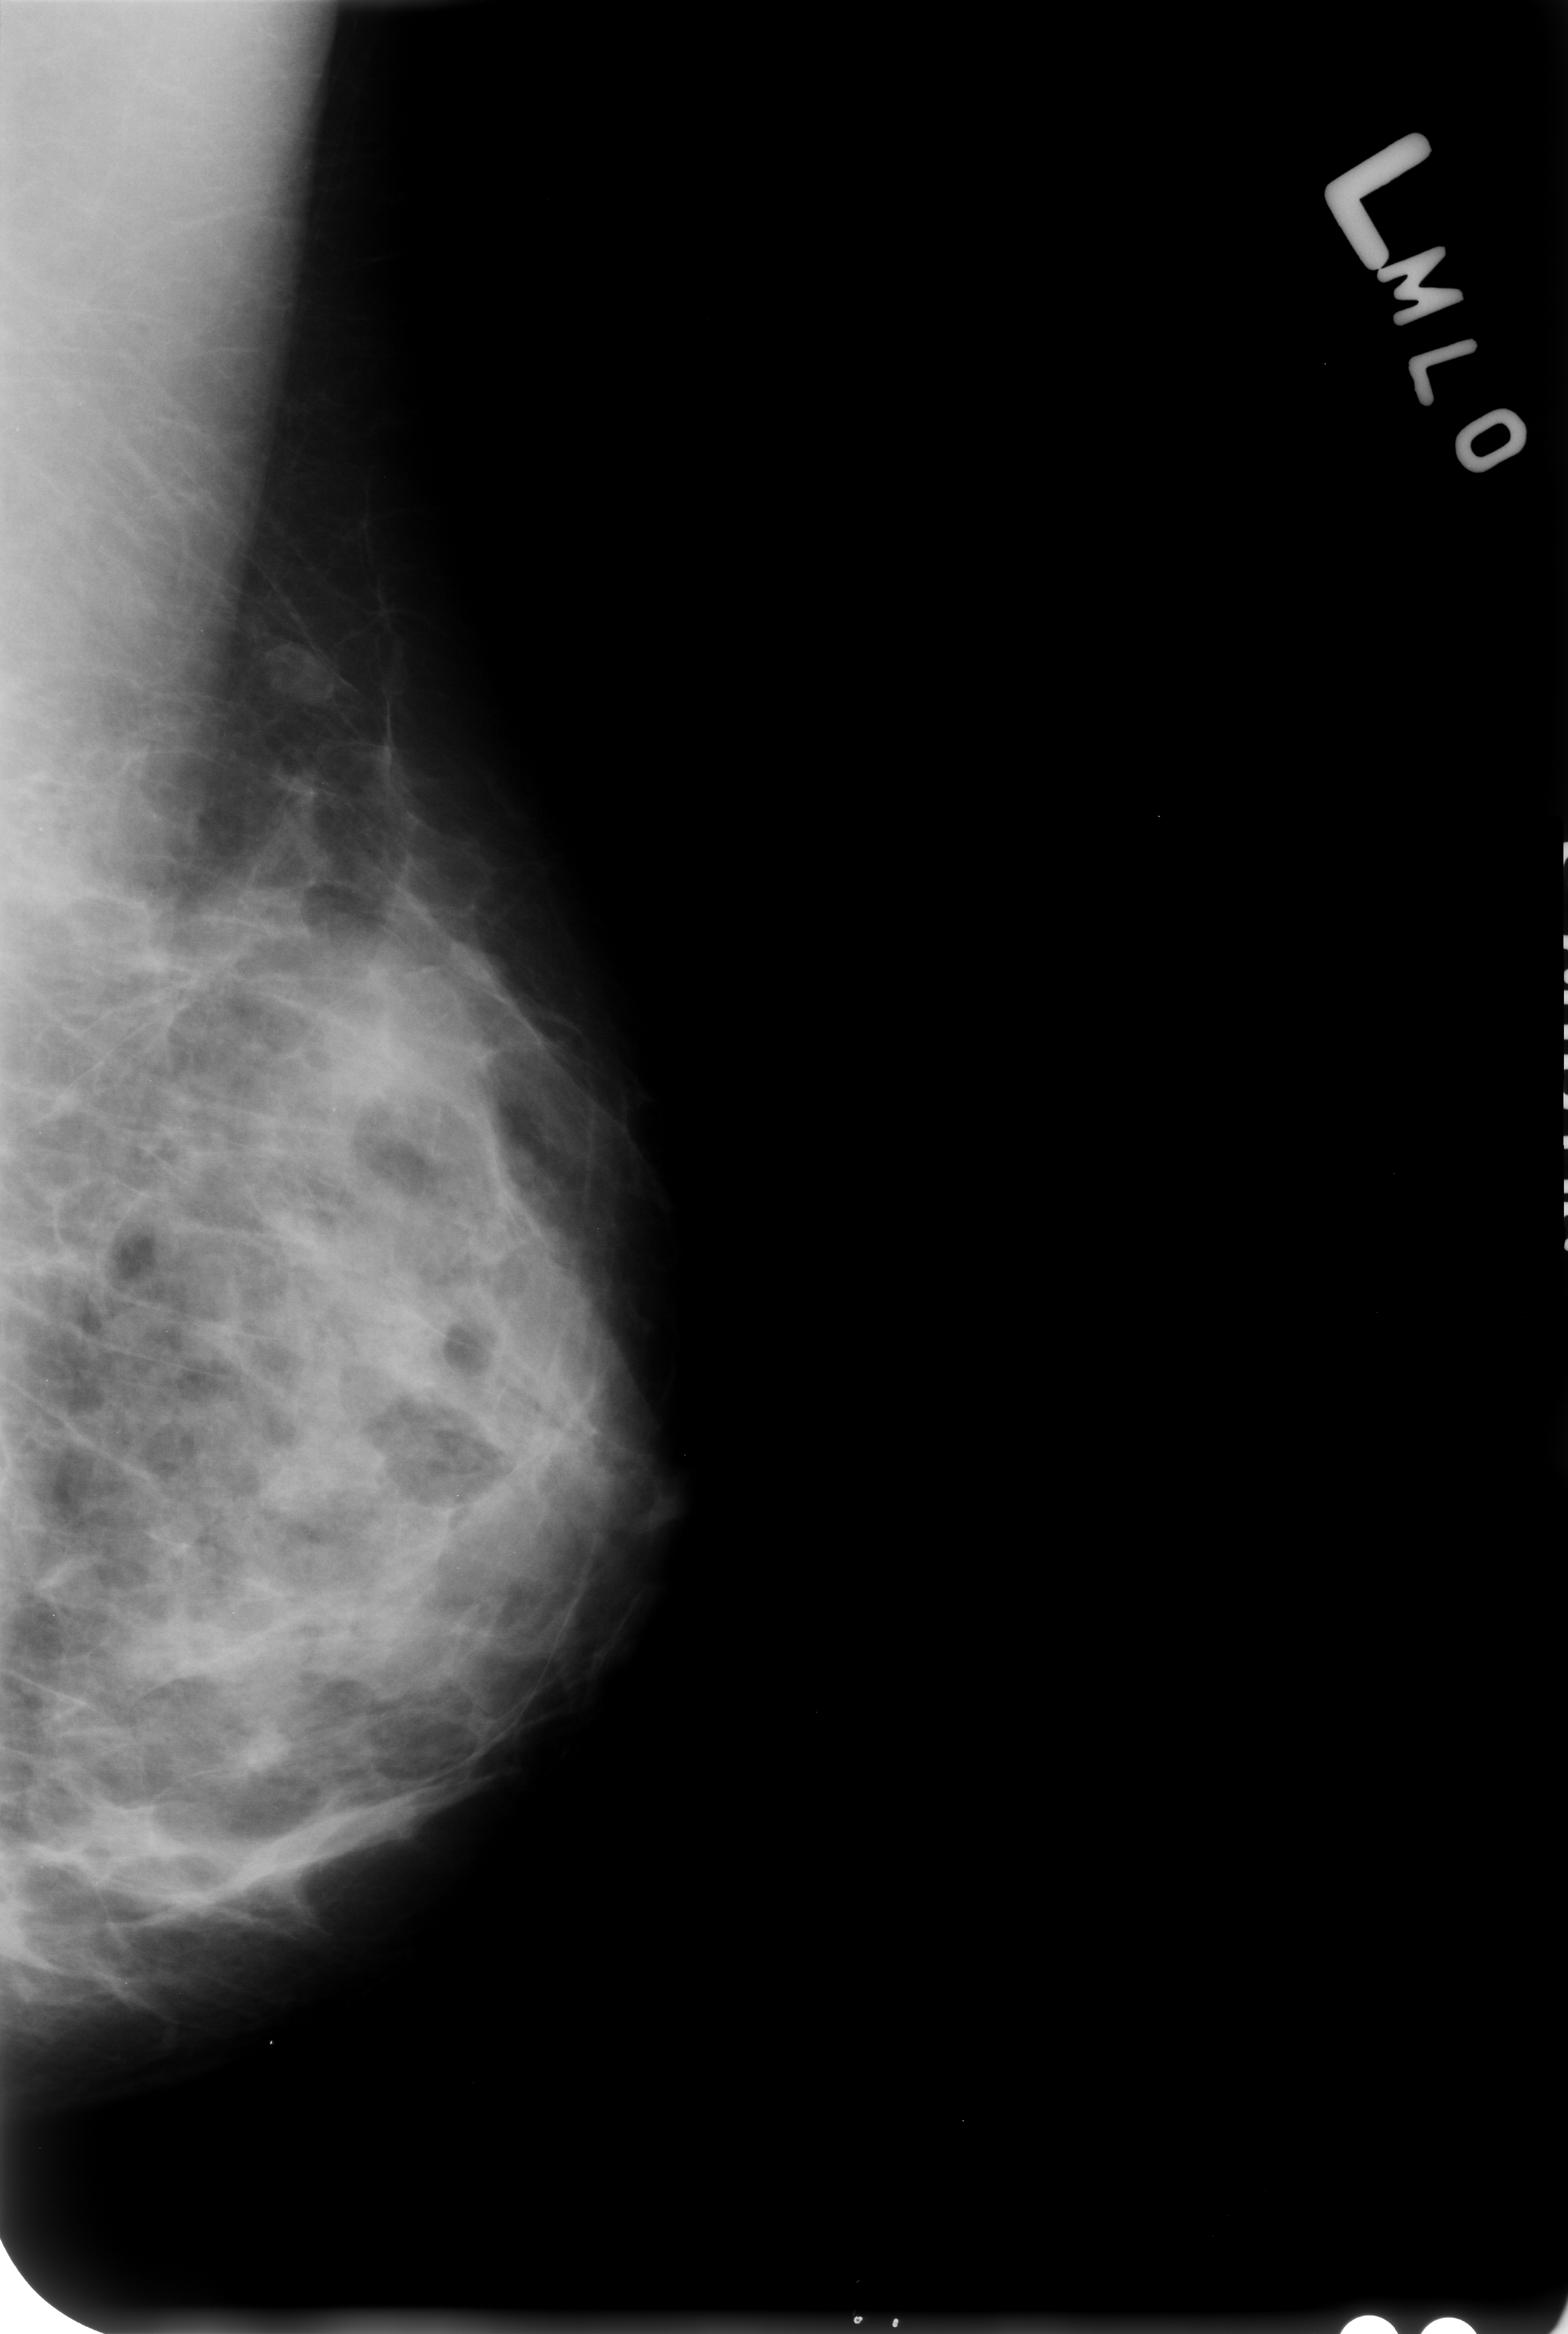
Digitized screen-film mammogram; left breast; mediolateral oblique (MLO) view; breast composition: heterogeneously dense (BI-RADS density category 3 of 4); 1568 × 2334 image matrix.
Expert-marked regions of interest on this film, with their recorded descriptors:
- calcifications, morphology punctate; BI-RADS assessment category 2; outcome (as recorded, no biopsy): benign without callback (not worked up further): bounding box [x1, y1, x2, y2] px = [281, 1112, 363, 1182]